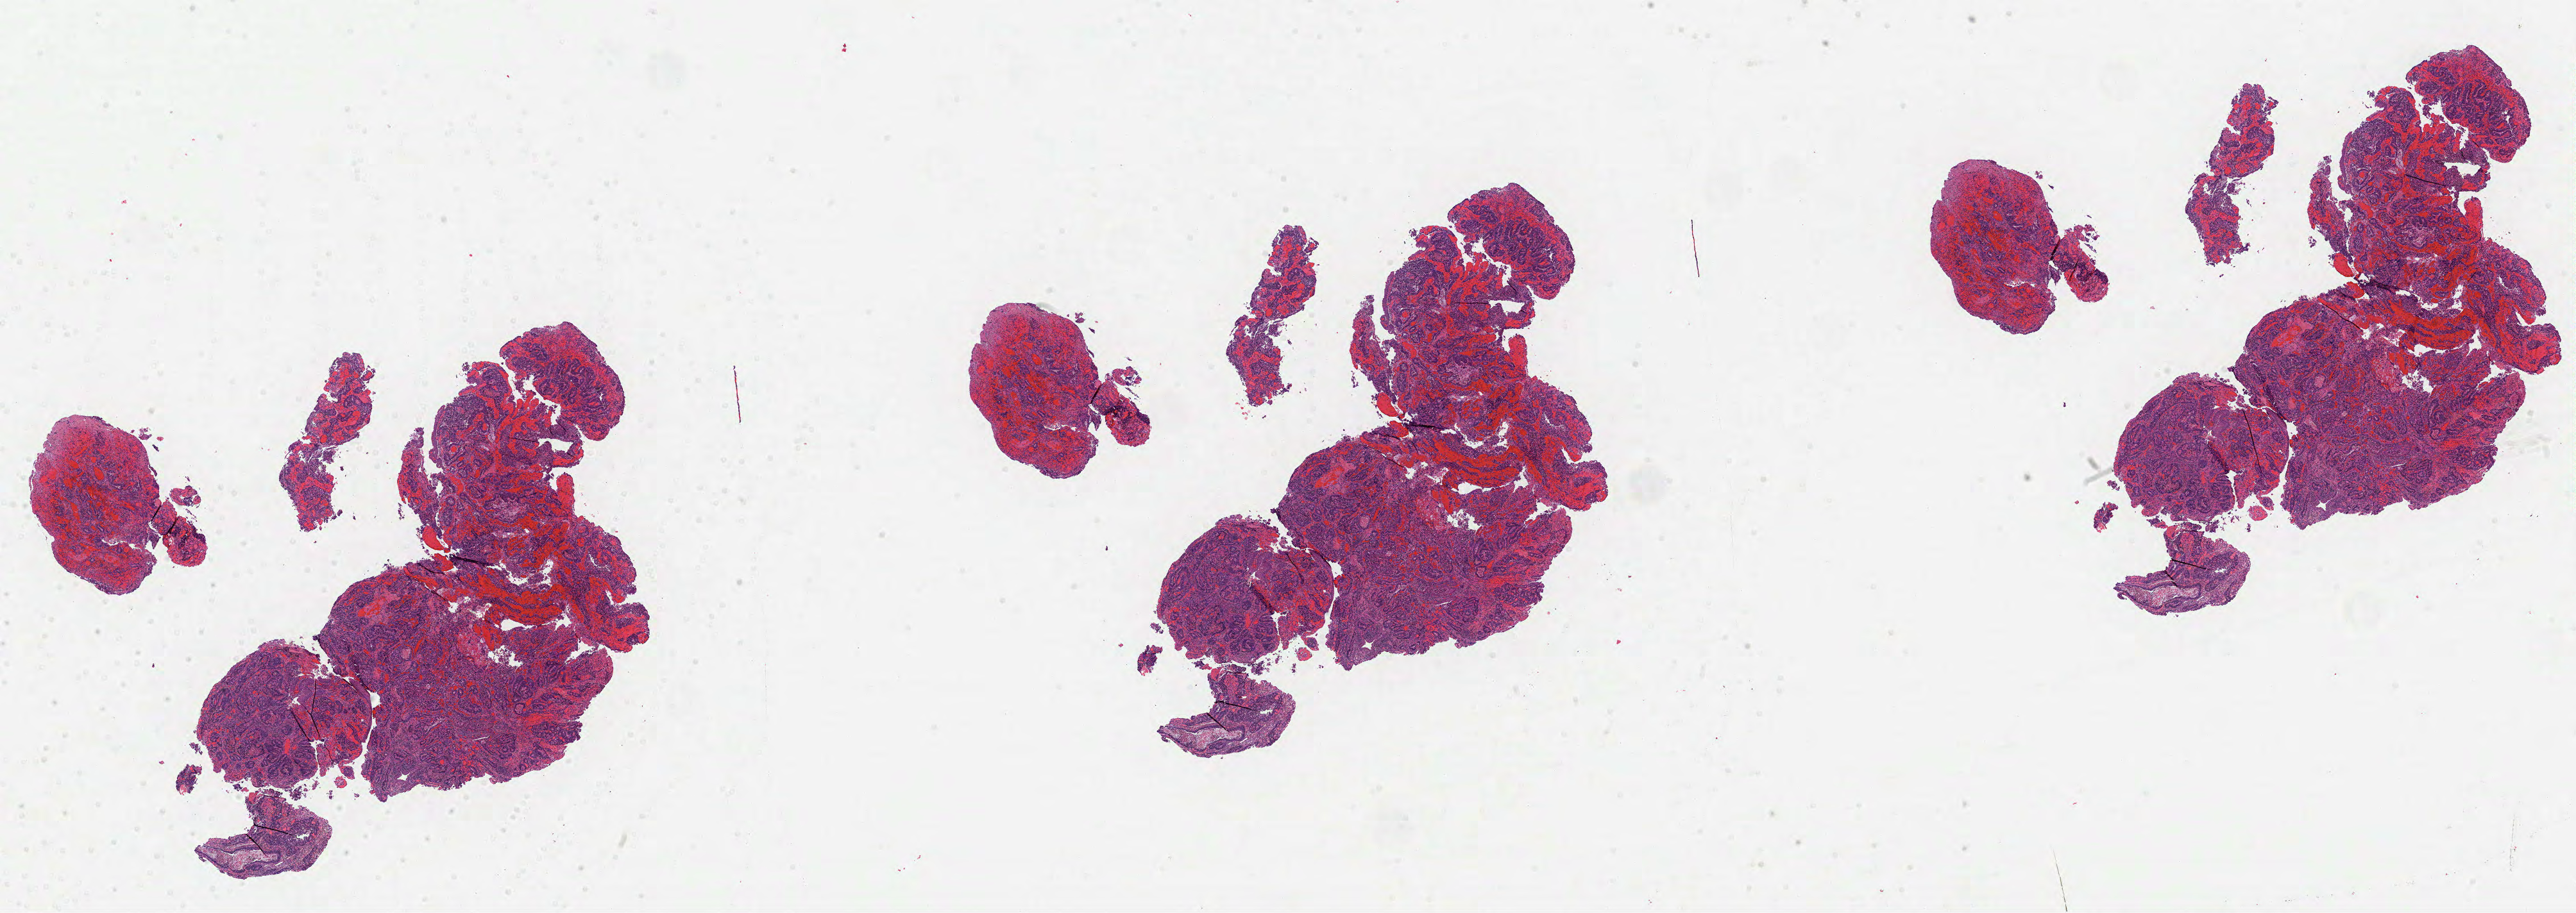
Digitized H&E-stained tissue section (whole slide) — whole scanned area (about 32.4 x 11.5 mm, acquisition: 40x scan) shown as a low-resolution overview. Formalin-fixed paraffin-embedded (FFPE) diagnostic section. Sample: primary tumour, stomach. Patient: male, age at initial diagnosis 74 years. Histologic grade: G2 (moderately differentiated).
- lymph nodes positive (case pathology): 4 of 49 examined
- AJCC pathologic stage: IIIB
- pathologic diagnosis: Signet ring cell carcinoma (cardia, NOS)
- TNM: T3 N2 MX